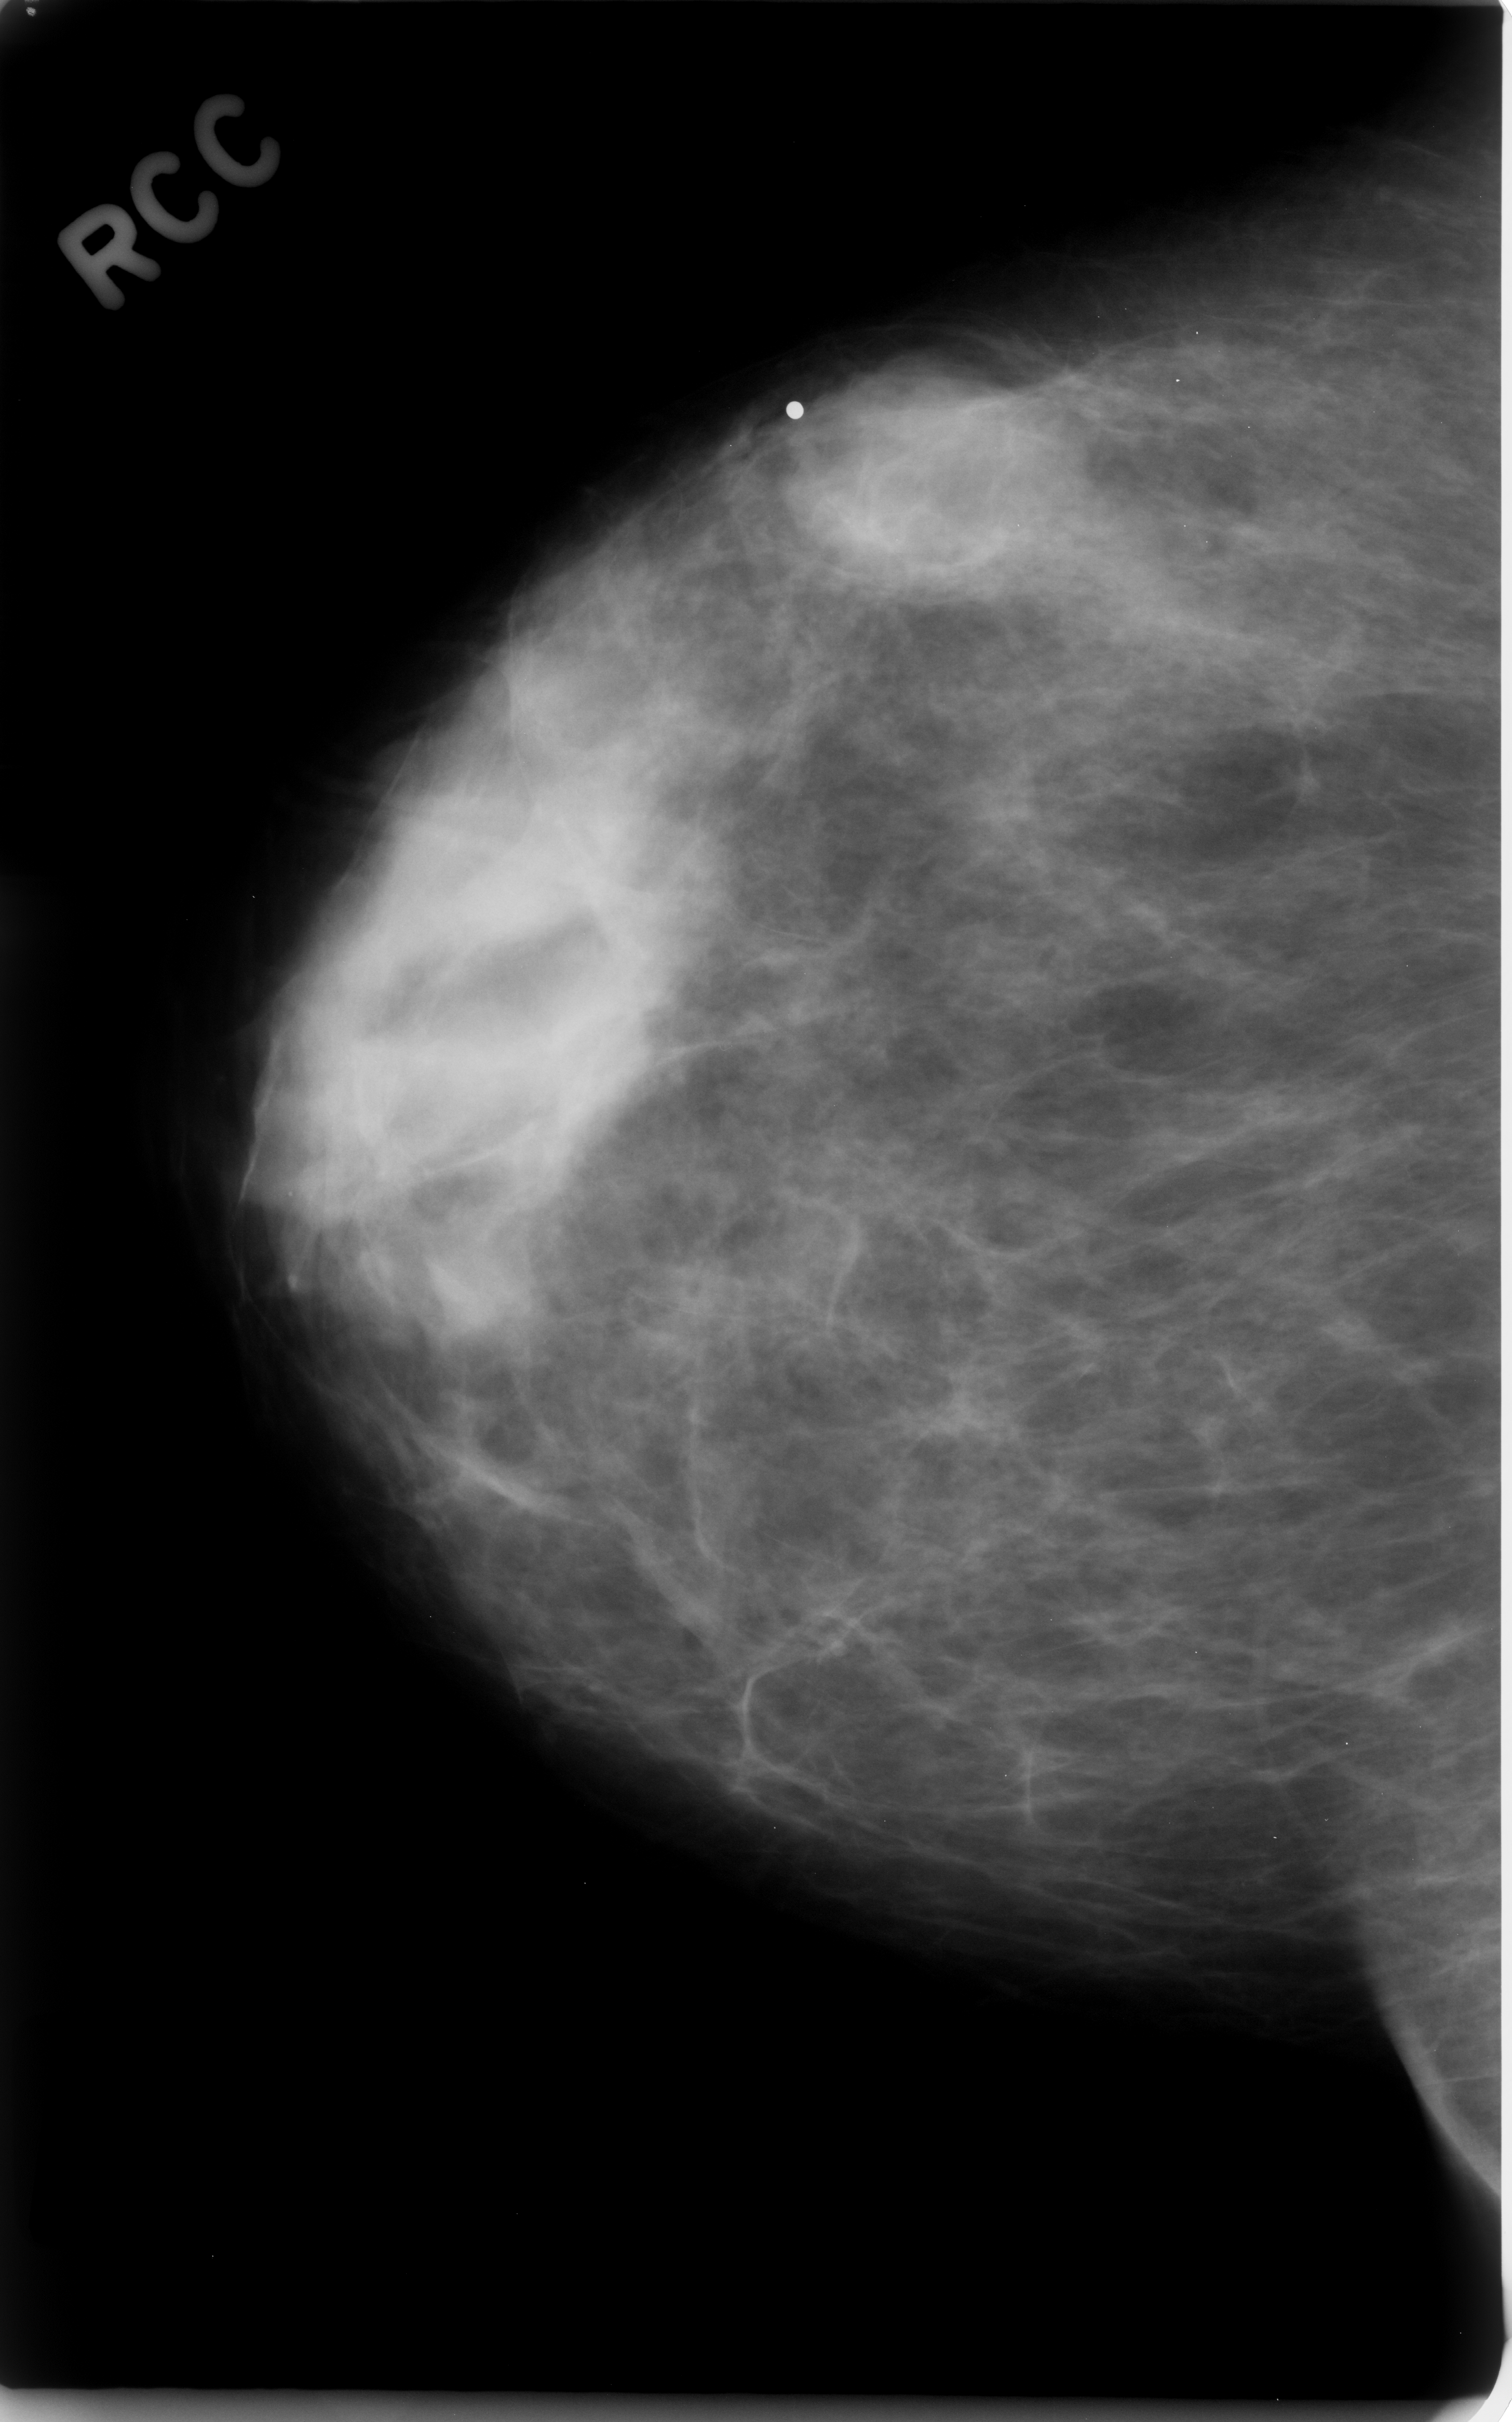
Mammogram (digitized film), right breast, CC view, breast composition: scattered fibroglandular densities (BI-RADS density category 2 of 4).
- Abnormality record for this image: mass, shape lobulated, margins obscured; BI-RADS assessment category 4; pathology result (as recorded, not read from the image): benign.